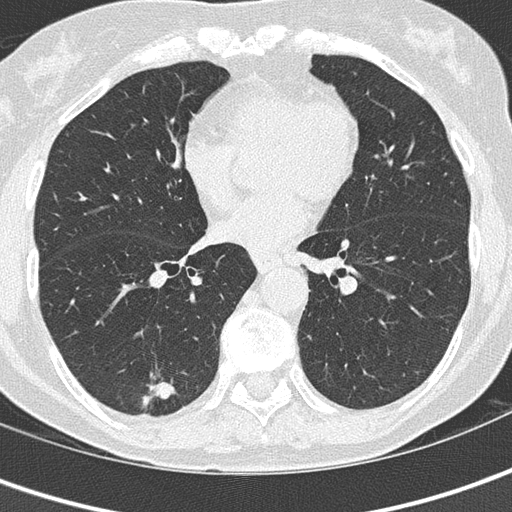
Axial slice from a low-dose chest CT screening exam, second screening round (one year after baseline), lung window (W 1500 / L -600 HU), 2 mm slice thickness, 120 kVp, 512 × 512 image matrix, field of view 280 × 280 mm. Female participant, aged 69 years at enrolment. Current smoker at enrolment.
- Expert reader's lesion annotation, bounding box (x1, y1, x2, y2) in pixels: (121, 363, 182, 424).
- The screening reader recorded 2 non-calcified nodules or masses ≥4 mm on this exam; which of them this box marks is not recorded.
- Later outcome: lung cancer diagnosed 112 days after this screen — adenocarcinoma, NOS, right lower lobe, moderately differentiated (G2), stage IA (AJCC 6th edition), 16 mm at pathology.